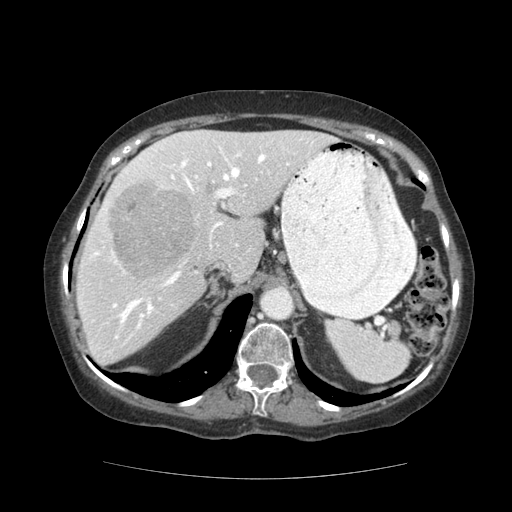
Contrast-enhanced abdominal CT (liver protocol), one axial slice; reconstruction kernel STANDARD; soft-tissue window (W 400 / L 40 HU); 512 × 512 image matrix, field of view 360 × 360 mm. Case-level facts recorded for this patient, not image findings: diagnosis: hepatocellular carcinoma (patient treated with transarterial chemoembolisation; whether this scan precedes or follows treatment is not stated here); TNM stage (as recorded): Stage-I; Child-Pugh class: A; tumour nodularity: uninodular; tumour size: 7.3 cm.
Outlined on this slice (semi-automatically segmented with operator editing):
- liver parenchyma outside the tumour (the mass and vessels are separate outlines, so this box may not span the whole liver): bounding box (x1, y1, x2, y2) in pixels: (76, 130, 332, 366)
- mass: (111, 182, 195, 276)
- liver vessels: (89, 133, 314, 339)